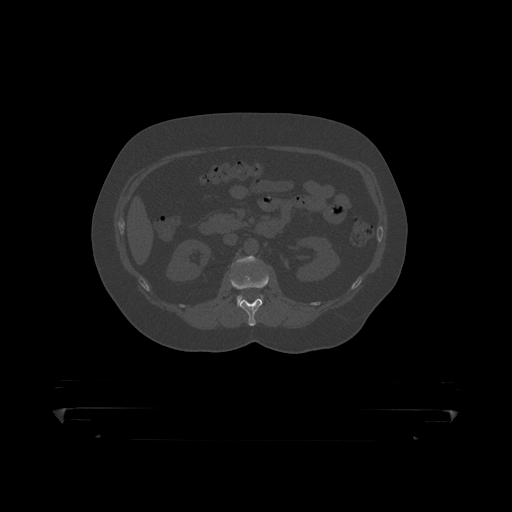
CT including the spine, one axial slice. Reconstruction kernel STANDARD. Bone window (W 1800 / L 400 HU). 1.25 mm slice thickness. 512 × 512 image matrix, field of view 650 × 650 mm. Patient: male, 60 years. From the clinical record (not read from this slice): primary cancer: prostate.
Structures marked on this image (semi-automatically segmented with operator editing):
- L1 vertebra: bounding box [x1, y1, x2, y2] px = [230, 272, 269, 319]
- L2 vertebra: [234, 256, 264, 306]